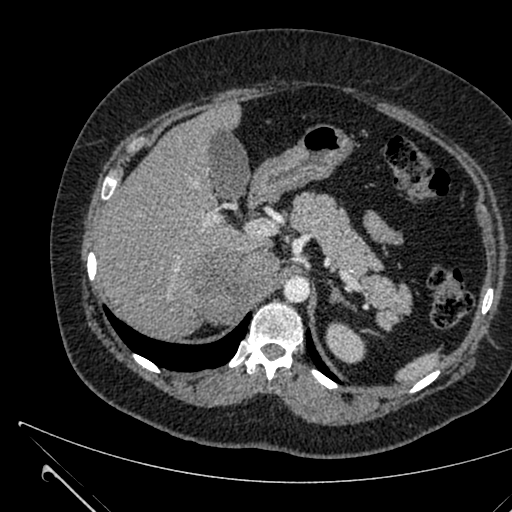
Contrast-enhanced abdominal CT, one axial slice. 120 kVp. Soft-tissue window (W 400 / L 40 HU). 1 mm slice thickness. 512 × 512 image matrix. Female patient, age 36 years. From the clinical record (not read from this slice): diagnosis: adrenocortical carcinoma; tumour side: right adrenal; tumour size at pathology: 10 cm; Ki-67 index: 20 %; stage (as recorded): 4.
Outlined on this slice (semi-automatically segmented with operator editing):
- mass: bounding box (x1, y1, x2, y2) in pixels: (199, 252, 278, 323)